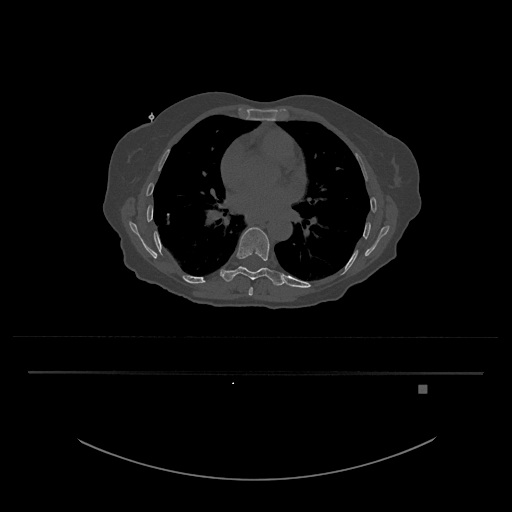
CT including the spine, one axial slice. Slice 761 of 797 in the series (ordered by position). Reconstruction kernel Br40s/3. 120 kVp. Bone window (W 1800 / L 400 HU). 0.5 mm slice thickness. 512 × 512 image matrix, field of view 500 × 500 mm. Patient: female, 57 years. From the clinical record (not read from this slice): primary cancer: cervical.
Outlined on this slice (semi-automatic segmentation, software-assisted and operator-edited):
- T8 vertebra: bounding box [x1, y1, x2, y2] px = [248, 287, 253, 296]
- T9 vertebra: [222, 227, 284, 286]